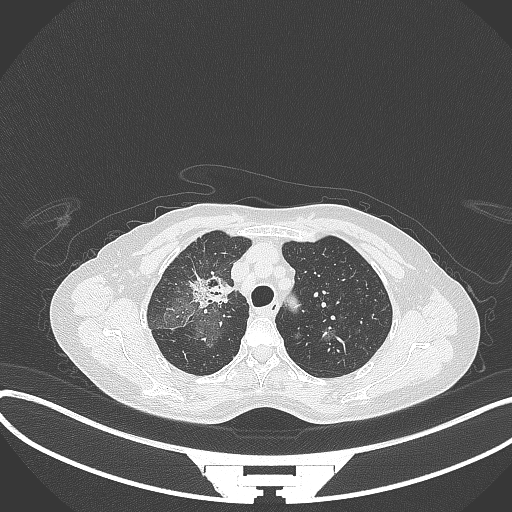
Chest CT, one axial slice; slice 244 of 284 in the series (ordered by position); 120 kVp; lung window (W 1500 / L -600 HU); 1 mm slice thickness; 512 × 512 image matrix. Patient: female, 59 years. From the clinical record (not read from this slice): clinical TNM (as recorded): T3 N0 M0.
Annotated regions visible in this slice (bounding box drawn by a radiologist):
- lung tumour (recorded histology: adenocarcinoma): bounding box <187,270,233,311> (left, top, right, bottom; pixels)